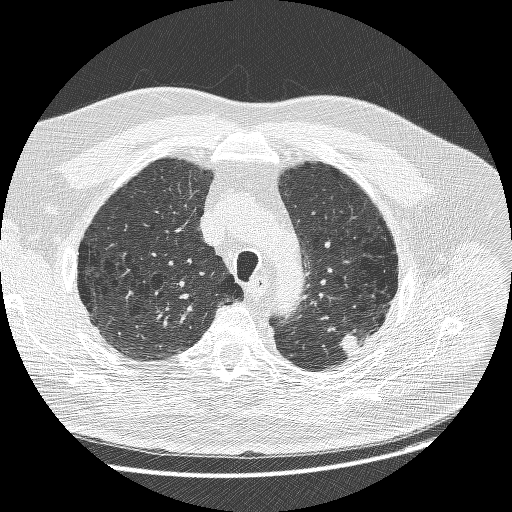
Chest CT (low-dose screening protocol), one axial image. Baseline screening round. Lung window (W 1500 / L -600 HU). 1.25 mm slice thickness. Slice 205 of 258 in the series. Male, age 68 years at enrolment. Former smoker at enrolment.
Expert-annotated lung lesion, box from (x=330, y=322) to (x=388, y=365) px. Screening reader's record for this exam (one nodule recorded; not confirmed to be the boxed lesion): non-calcified nodule or mass ≥4 mm, left upper lobe, 15 × 14 mm, smooth margins, soft tissue attenuation. Later outcome: lung cancer diagnosed 19 days after this screen — adenosquamous carcinoma, left upper lobe, poorly differentiated (G3), stage IIIB (AJCC 6th edition), 32 mm at pathology.